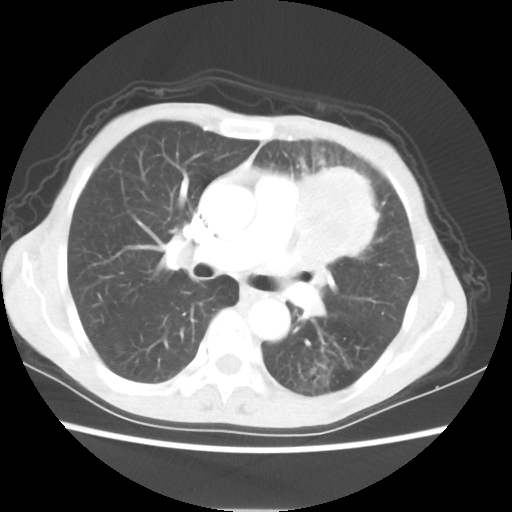
Chest CT, one axial slice; slice 34 of 56 in the series (ordered by position); reconstruction kernel STANDARD; 80 kVp; lung window (W 1500 / L -600 HU); 512 × 512 image matrix. Patient: female, 60 years. Case-level facts recorded for this patient, not image findings: clinical TNM (as recorded): T4 N1 M0.
Structures marked on this image (bounding box drawn by a radiologist):
- lung tumour (recorded histology: adenocarcinoma): bounding box <293,164,384,283> (left, top, right, bottom; pixels)